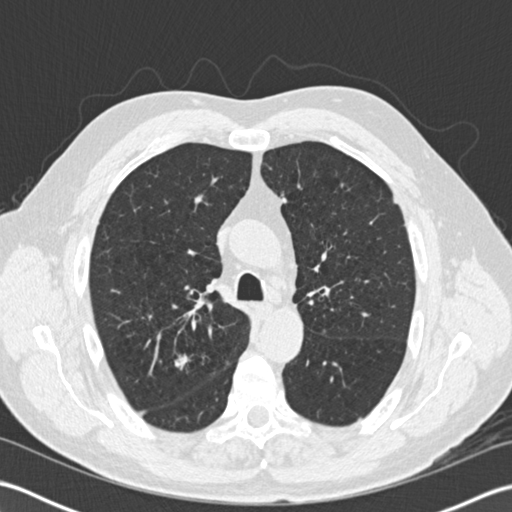
Low-dose screening chest CT, axial slice; second annual screen; lung window (W 1500 / L -600 HU); 2 mm slice thickness; standard (soft-tissue) reconstruction kernel (B30f); slice 56 of 204 in the series; 512 × 512 image matrix, field of view 350 × 350 mm. Male, age 65 years at enrolment. Former smoker at enrolment.
• Lesion marked by an expert reader, bounding box <158,348,202,385> (left, top, right, bottom; pixels).
• The screening reader recorded 6 non-calcified nodules or masses ≥4 mm on this exam (right upper lobe, left upper lobe, left upper lobe, right upper lobe, left upper lobe, right upper lobe); which of them this box marks is not recorded.
• Participant outcome: lung cancer diagnosed 421 days after this screen — adenocarcinoma, NOS, right upper lobe, moderately differentiated (G2), stage IA (AJCC 6th edition), 16 mm at pathology.